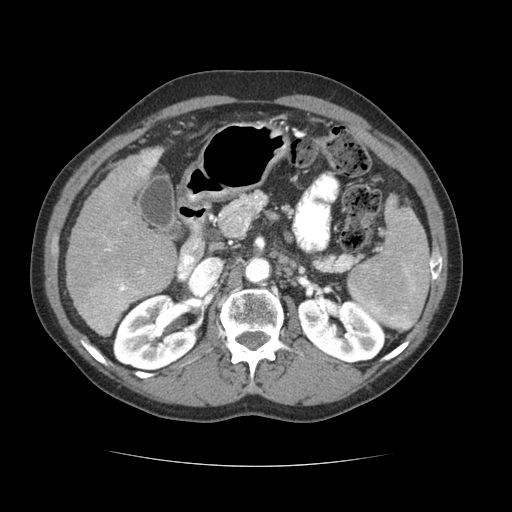
Contrast-enhanced abdominal CT (liver protocol), one axial slice; position 34 of 69 along the scan axis; reconstruction kernel STANDARD; soft-tissue window (W 400 / L 40 HU); 2.5 mm slice thickness; 512 × 512 image matrix, field of view 360 × 360 mm. From the clinical record (not read from this slice): diagnosis: hepatocellular carcinoma (patient treated with transarterial chemoembolisation; whether this scan precedes or follows treatment is not stated here); TNM stage (as recorded): Stage-II; Child-Pugh class: B; tumour differentiation: poorly differentiated; tumour nodularity: multinodular.
Annotated regions visible in this slice (semi-automatic segmentation, software-assisted and operator-edited):
- liver parenchyma outside the tumour (the mass and vessels are separate outlines, so this box may not span the whole liver): box from (x=66, y=148) to (x=176, y=332) px
- mass: (x=79, y=272)–(x=139, y=336)
- liver vessels: (x=105, y=150)–(x=160, y=273)